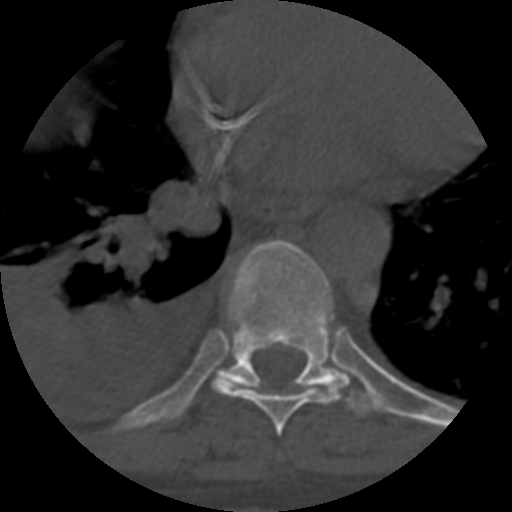
CT including the spine, one axial slice. Reconstruction kernel STANDARD. 120 kVp. One of 3 acquisitions stored at this slice position. Bone window (W 1800 / L 400 HU). 1.25 mm slice thickness. 512 × 512 image matrix, field of view 160 × 160 mm. Patient age 55 years. Case-level facts recorded for this patient, not image findings: primary cancer: colon; vertebrae with lytic lesions (as recorded): T12, L1, L5.
Outlined on this slice (semi-automatic segmentation, software-assisted and operator-edited):
- T8 vertebra: bounding box [x1, y1, x2, y2] px = [212, 376, 346, 436]
- T9 vertebra: [218, 241, 369, 417]